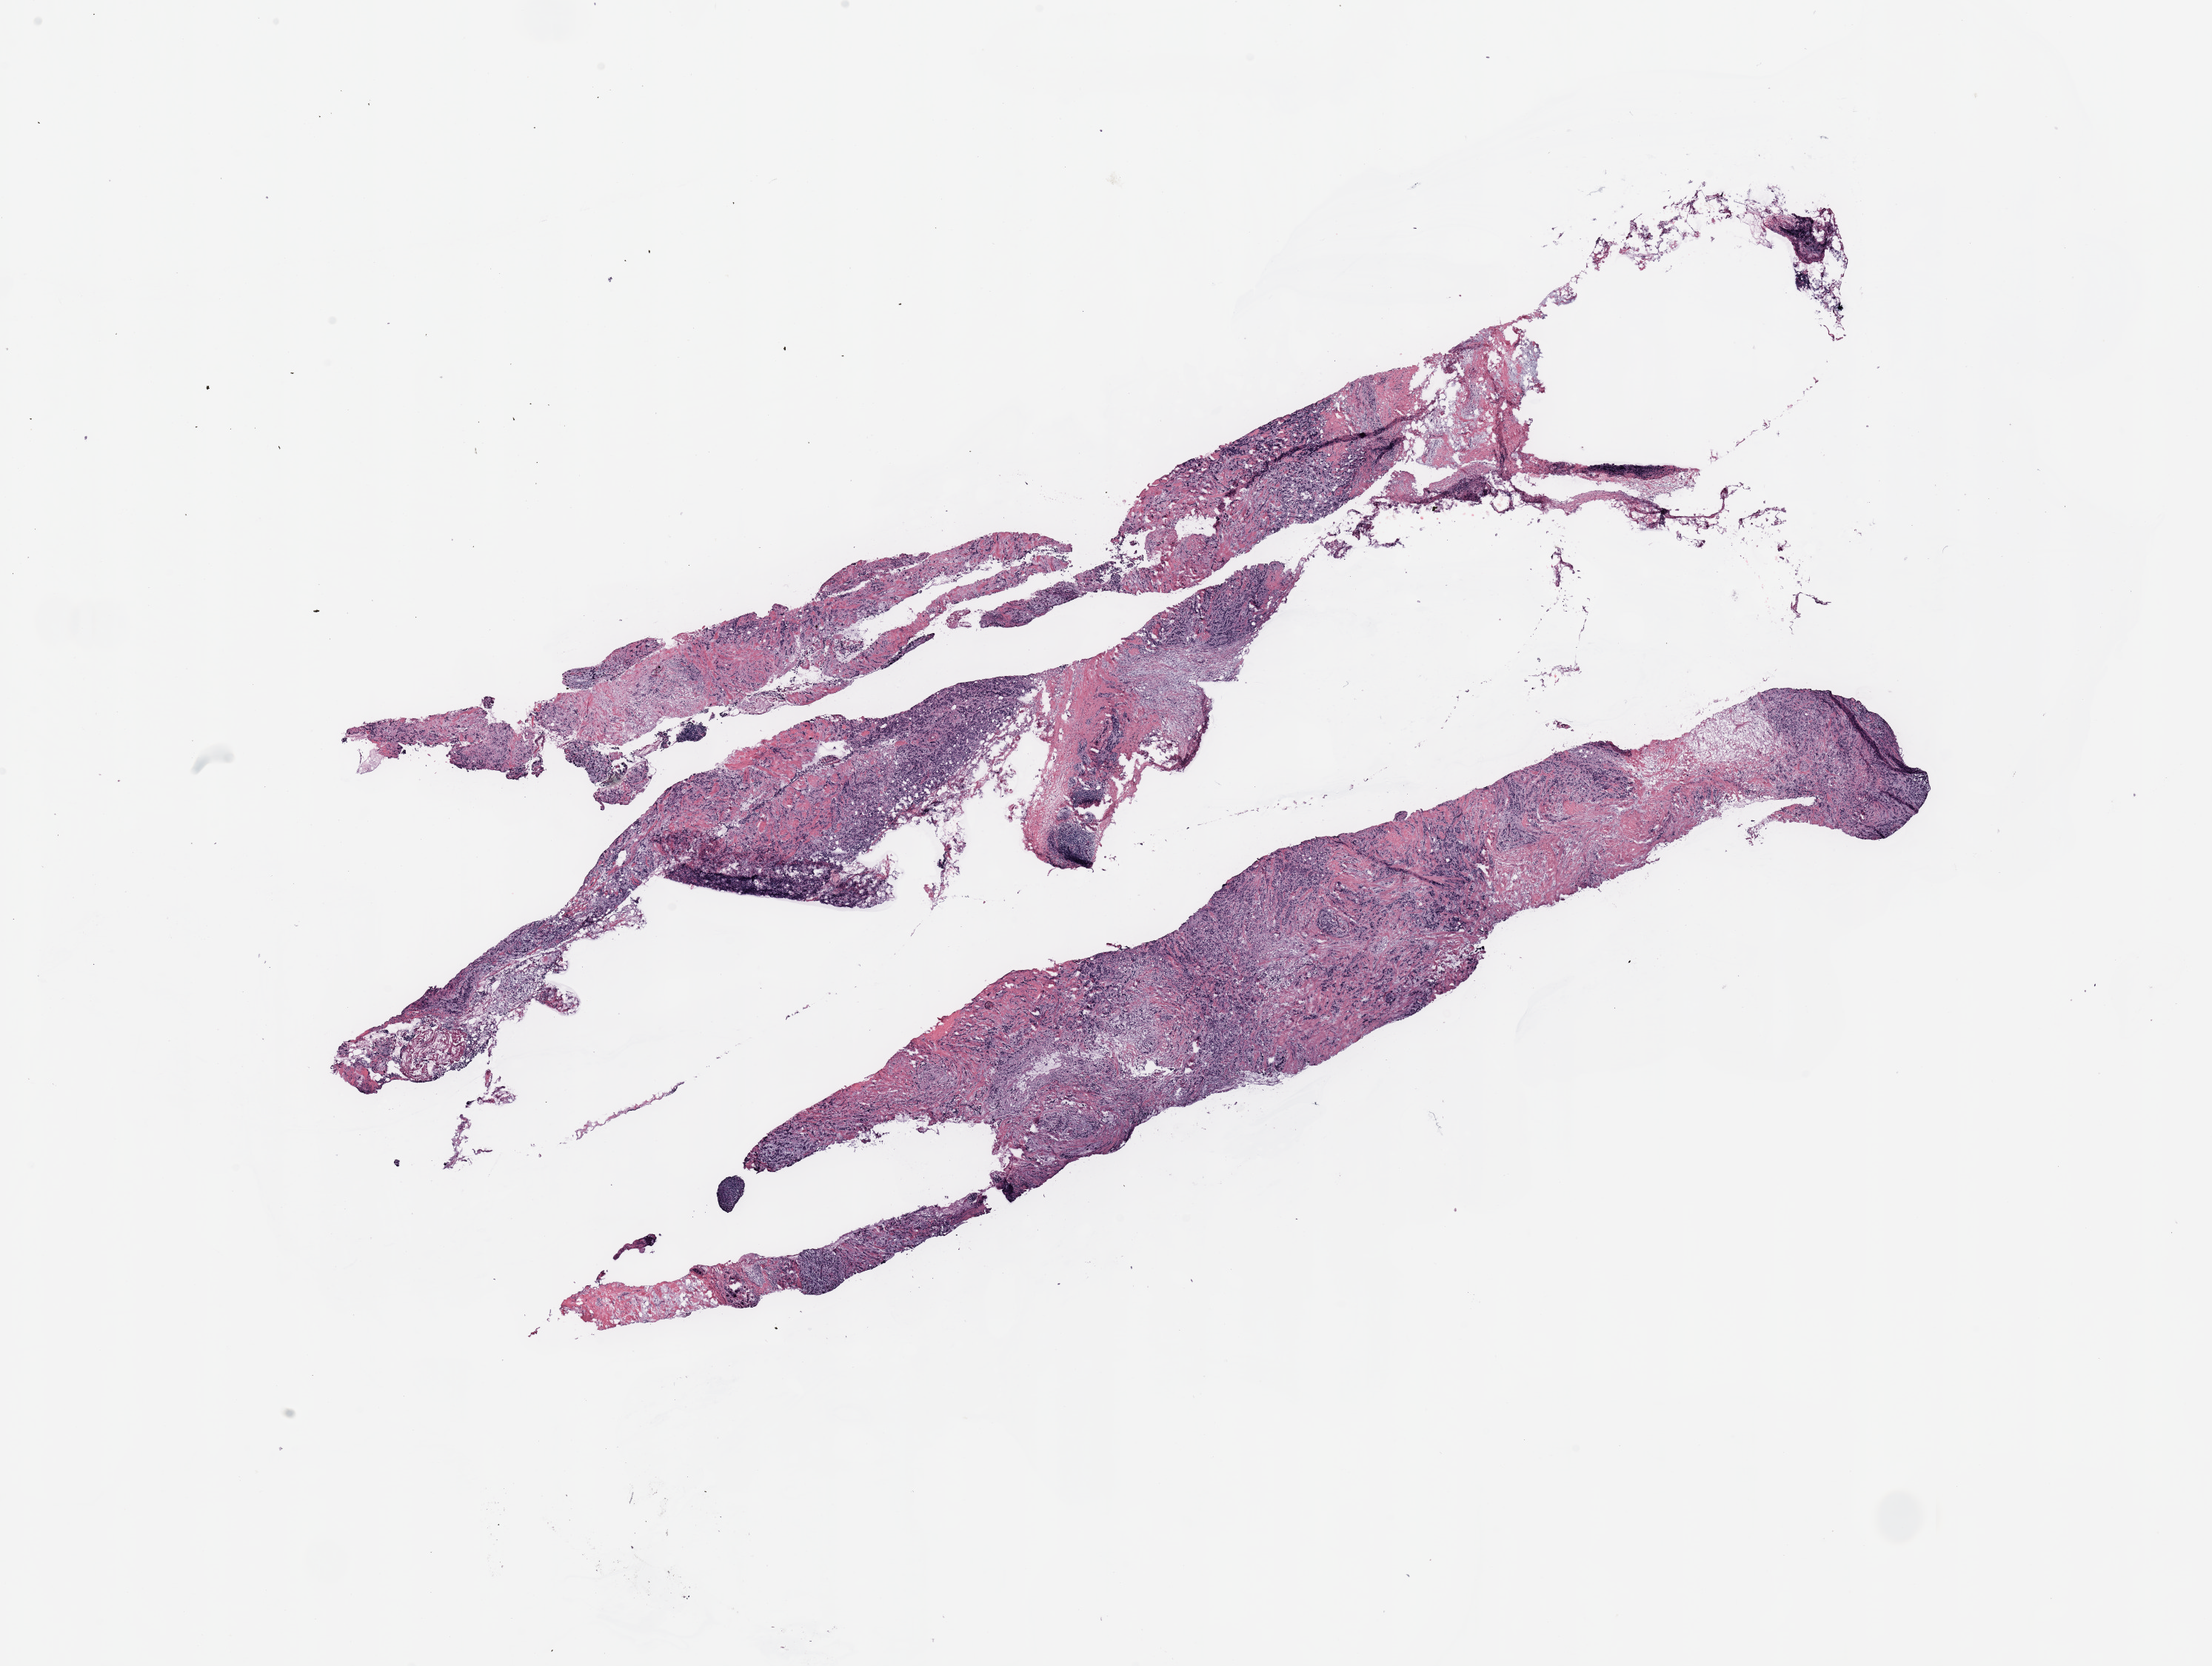
H&E whole-slide image, shown as a low-resolution overview of the whole scanned area (about 23.6 x 17.8 mm, acquisition: 20x scan). Breast, tissue type not recorded.
Patient diagnosis (cohort enrolment): breast cancer (breast).